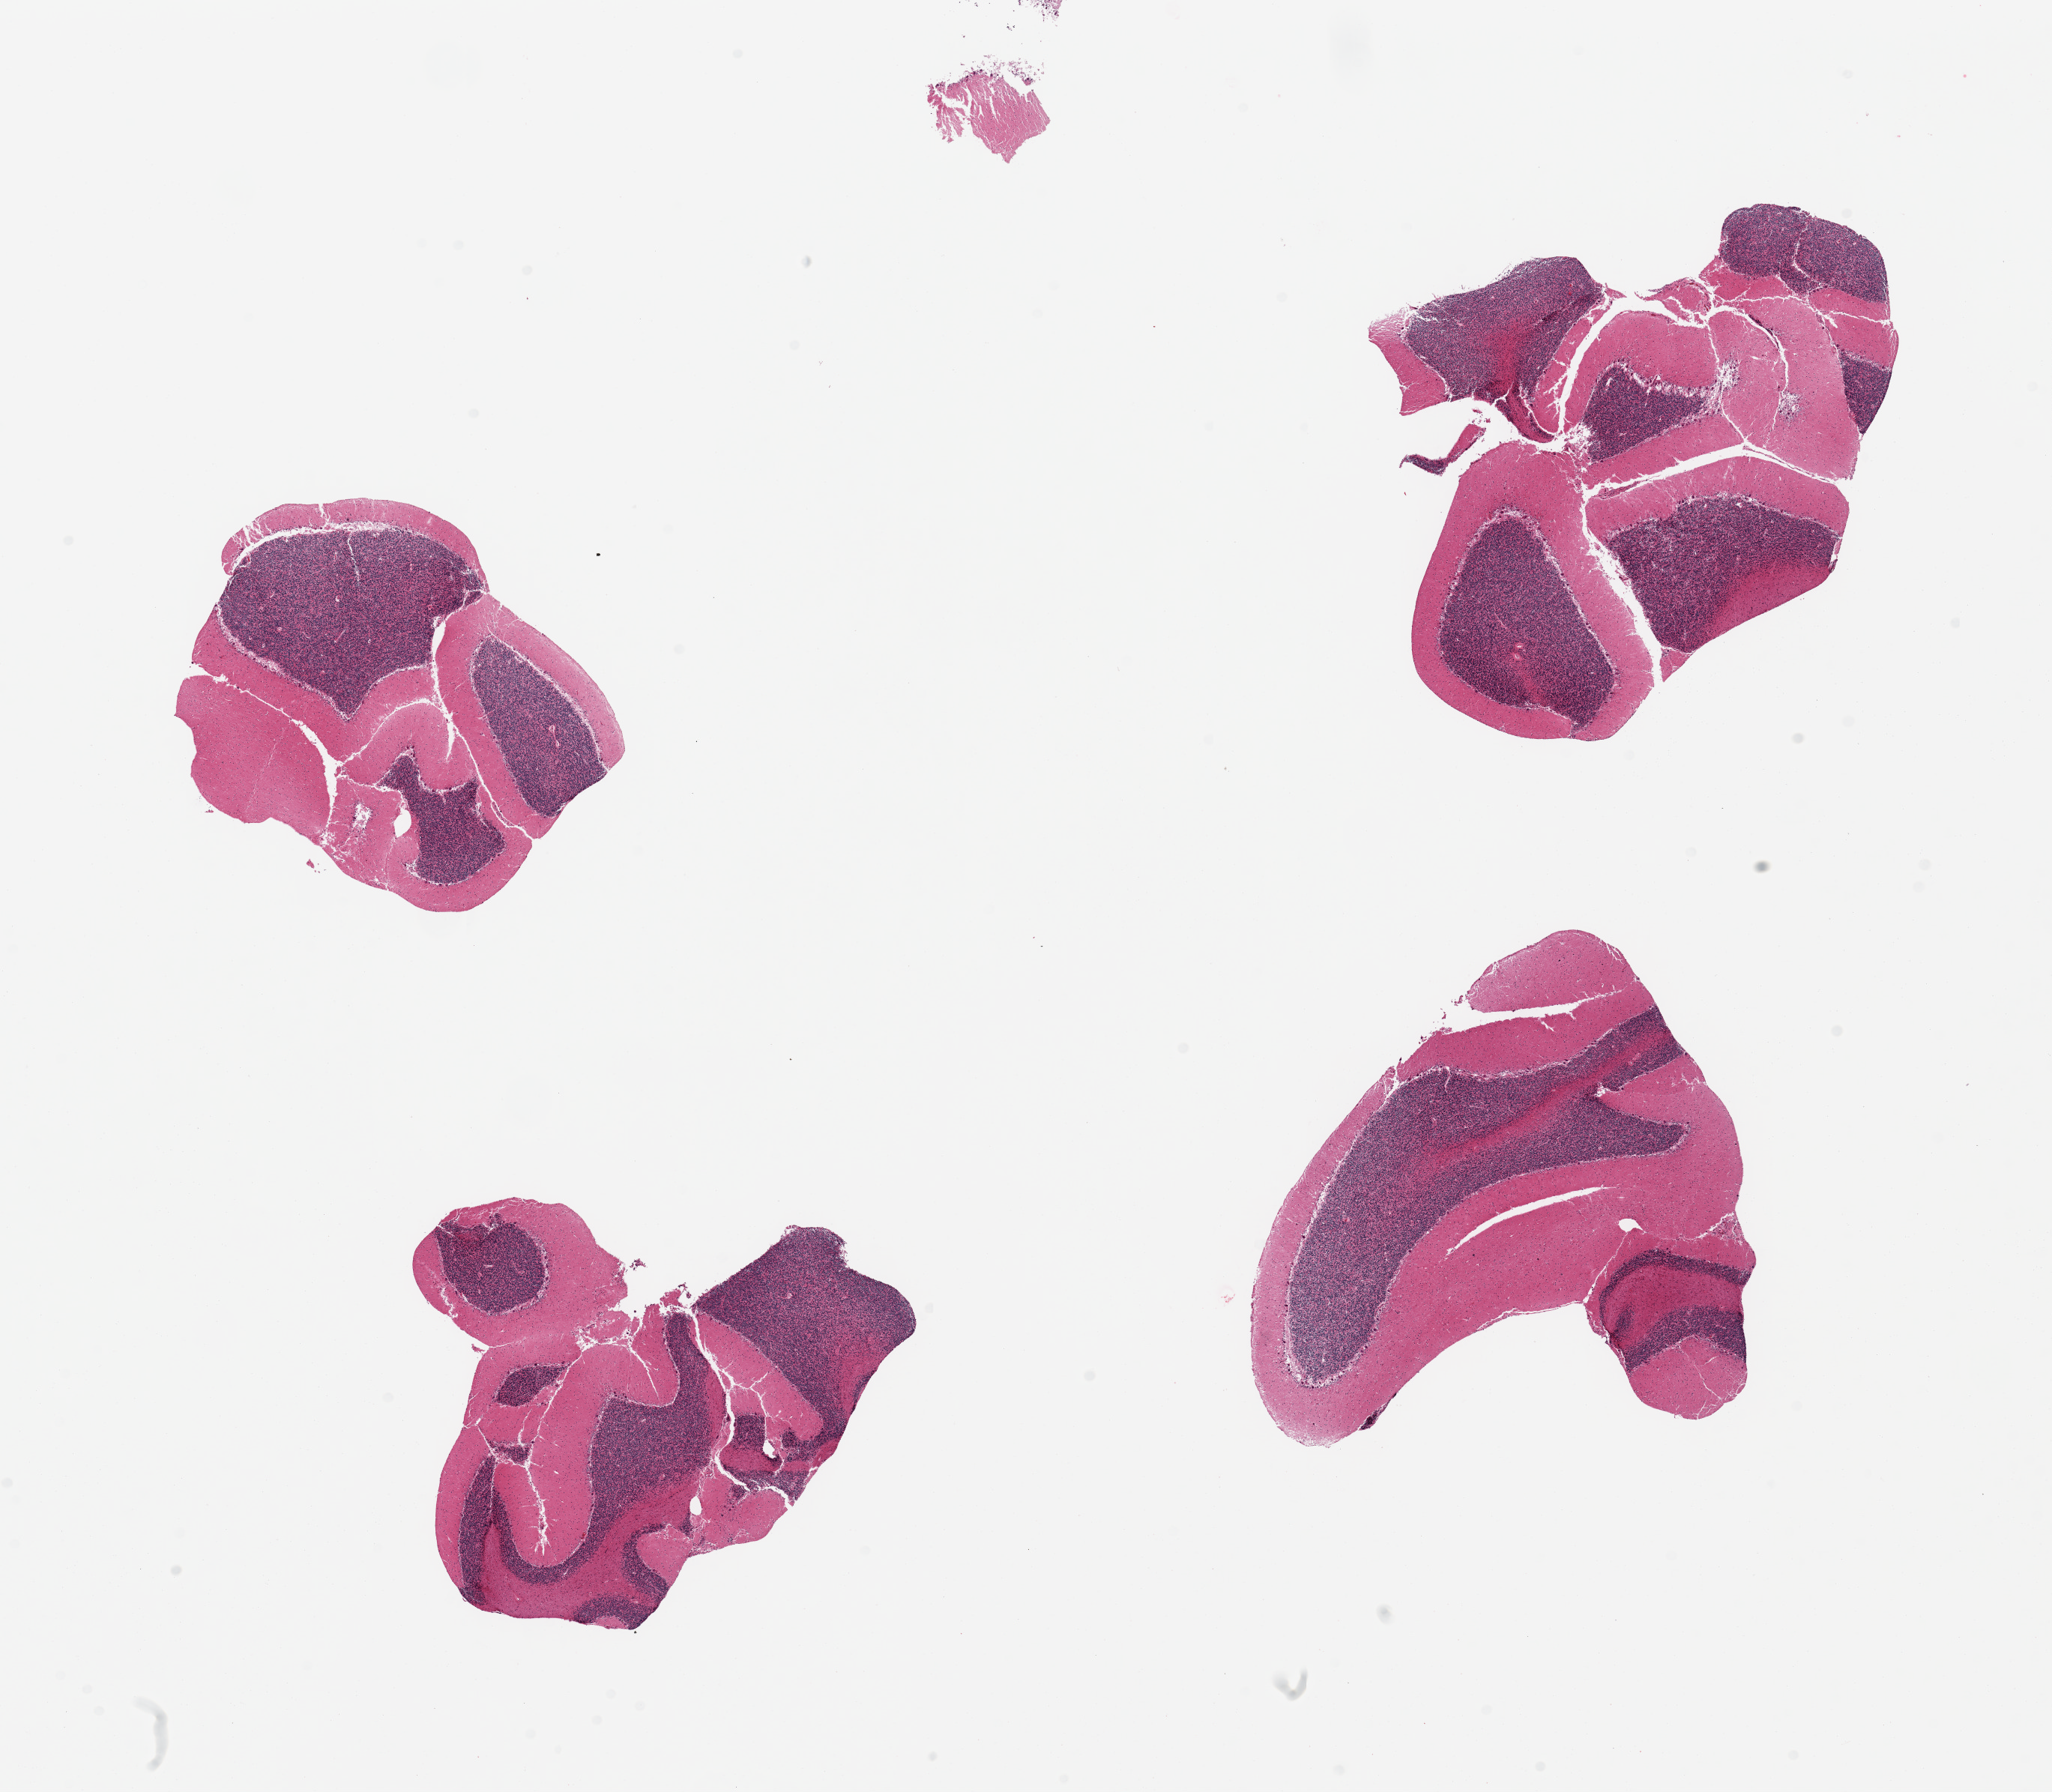
Digitized H&E-stained section, a low-resolution overview of the entire scanned area, about 21.7 x 18.9 mm (acquisition: 20x scan); PAXgene-fixed paraffin-embedded (PFPE) section; section of cerebellum (target tissue); tissue donor sample. Donor: female.
Reviewer comment on this tissue sample: 4 pieces.